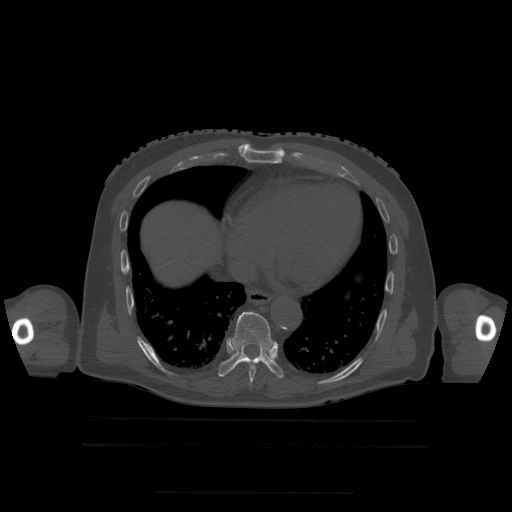
CT including the spine, one axial slice. Position 267 of 522 along the scan axis. Bone window (W 1800 / L 400 HU). 1.25 mm slice thickness. 512 × 512 image matrix, field of view 436 × 436 mm. Patient age 68 years. From the clinical record (not read from this slice): primary cancer: urothelial.
Structures marked on this image (semi-automatically segmented with operator editing):
- T7 vertebra: bounding box (x1, y1, x2, y2) in pixels: (250, 382, 253, 385)
- T8 vertebra: (249, 364, 257, 382)
- T9 vertebra: (218, 312, 284, 379)